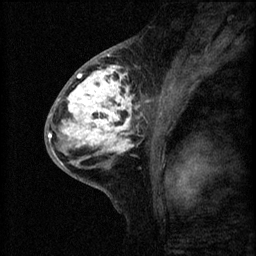
Breast MRI (dynamic contrast-enhanced), one sagittal slice. Position 31 of 60 along the scan axis. 3 images stored at this slice position (order not interpretable as contrast timing). 1.5 T. TE 4.2 ms, TR 8.2 ms. 2 mm slice thickness. 256 × 256 image matrix, field of view 180 × 180 mm. Female patient, age 41 years.
Structures marked on this image (semi-automatically segmented with operator editing):
- analysis volume of interest (the breast-tissue region the enhancement analysis was run in; not a lesion): bounding box <53,62,160,175> (left, top, right, bottom; pixels)
- tumour enhancement mask (voxels above the 70 % enhancement threshold inside the analysis volume of interest): <53,66,149,167>